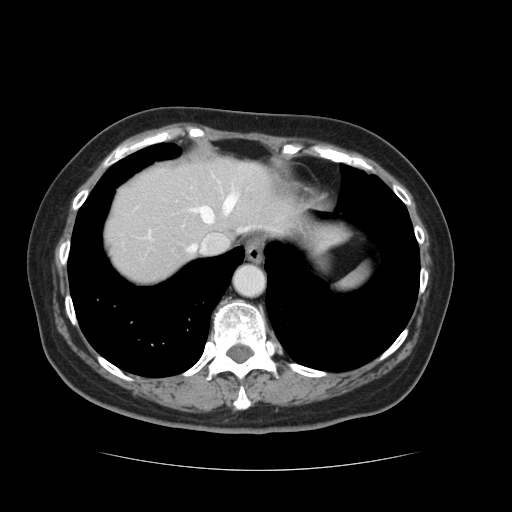
Contrast-enhanced abdominal CT, one axial slice. 120 kVp. Intravenous contrast given. Soft-tissue window (W 400 / L 40 HU). 2.5 mm slice thickness. 512 × 512 image matrix, field of view 366 × 366 mm. Female patient, age 67 years. From the clinical record (not read from this slice): diagnosis: colorectal cancer liver metastases, imaged before liver resection; multiple liver metastases: yes; largest metastasis: 3 cm; disease in both lobes: yes.
Annotated regions visible in this slice (outlined manually by an expert reader):
- hepatic veins: bounding box <186,193,255,253> (left, top, right, bottom; pixels)
- liver: <103,157,291,284>
- planned liver remnant (the part of the liver to remain after resection): <103,159,292,284>